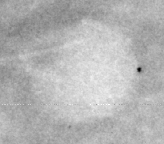
Region of interest cut from a scanned film mammogram (one marked finding); right breast; CC view; BI-RADS breast density category 1 (scale 1–4).
Marked abnormality: mass, shape lymph node, margins circumscribed; BI-RADS assessment category 2; benign without callback (not worked up further).